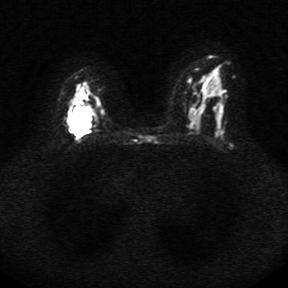
Breast MRI, one axial slice. Slice 20 of 34 in the series (ordered by position). Diffusion-weighted series; image 2 of 4 stored at this slice position (different b-values; order by instance number). 1.5 T. 5 mm slice thickness. 288 × 288 image matrix, field of view 340 × 340 mm. Female patient.
Outlined on this slice (manually delineated by an expert):
- tumour on diffusion-weighted imaging: bounding box <66,105,92,134> (left, top, right, bottom; pixels)